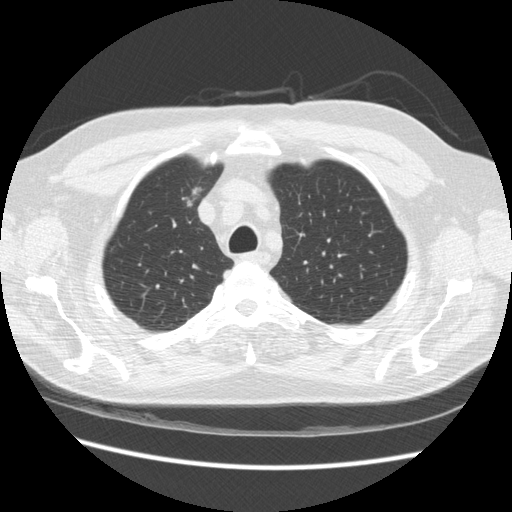
Low-dose screening chest CT, axial slice; third annual screen; lung window (W 1500 / L -600 HU); 2.5 mm slice thickness; slice 51 of 234 in the series. Male, age 66 years at enrolment.
- Expert-annotated lung lesion, bounding box (x1, y1, x2, y2) in pixels: (165, 175, 214, 219).
- No non-calcified nodule or mass ≥4 mm was recorded by the screening reader at this exam.
- Lung cancer was diagnosed 229 days after this screen: bronchiolo-alveolar adenocarcinoma, NOS, right upper lobe, moderately differentiated (G2), stage IA (AJCC 6th edition), 12 mm at pathology.